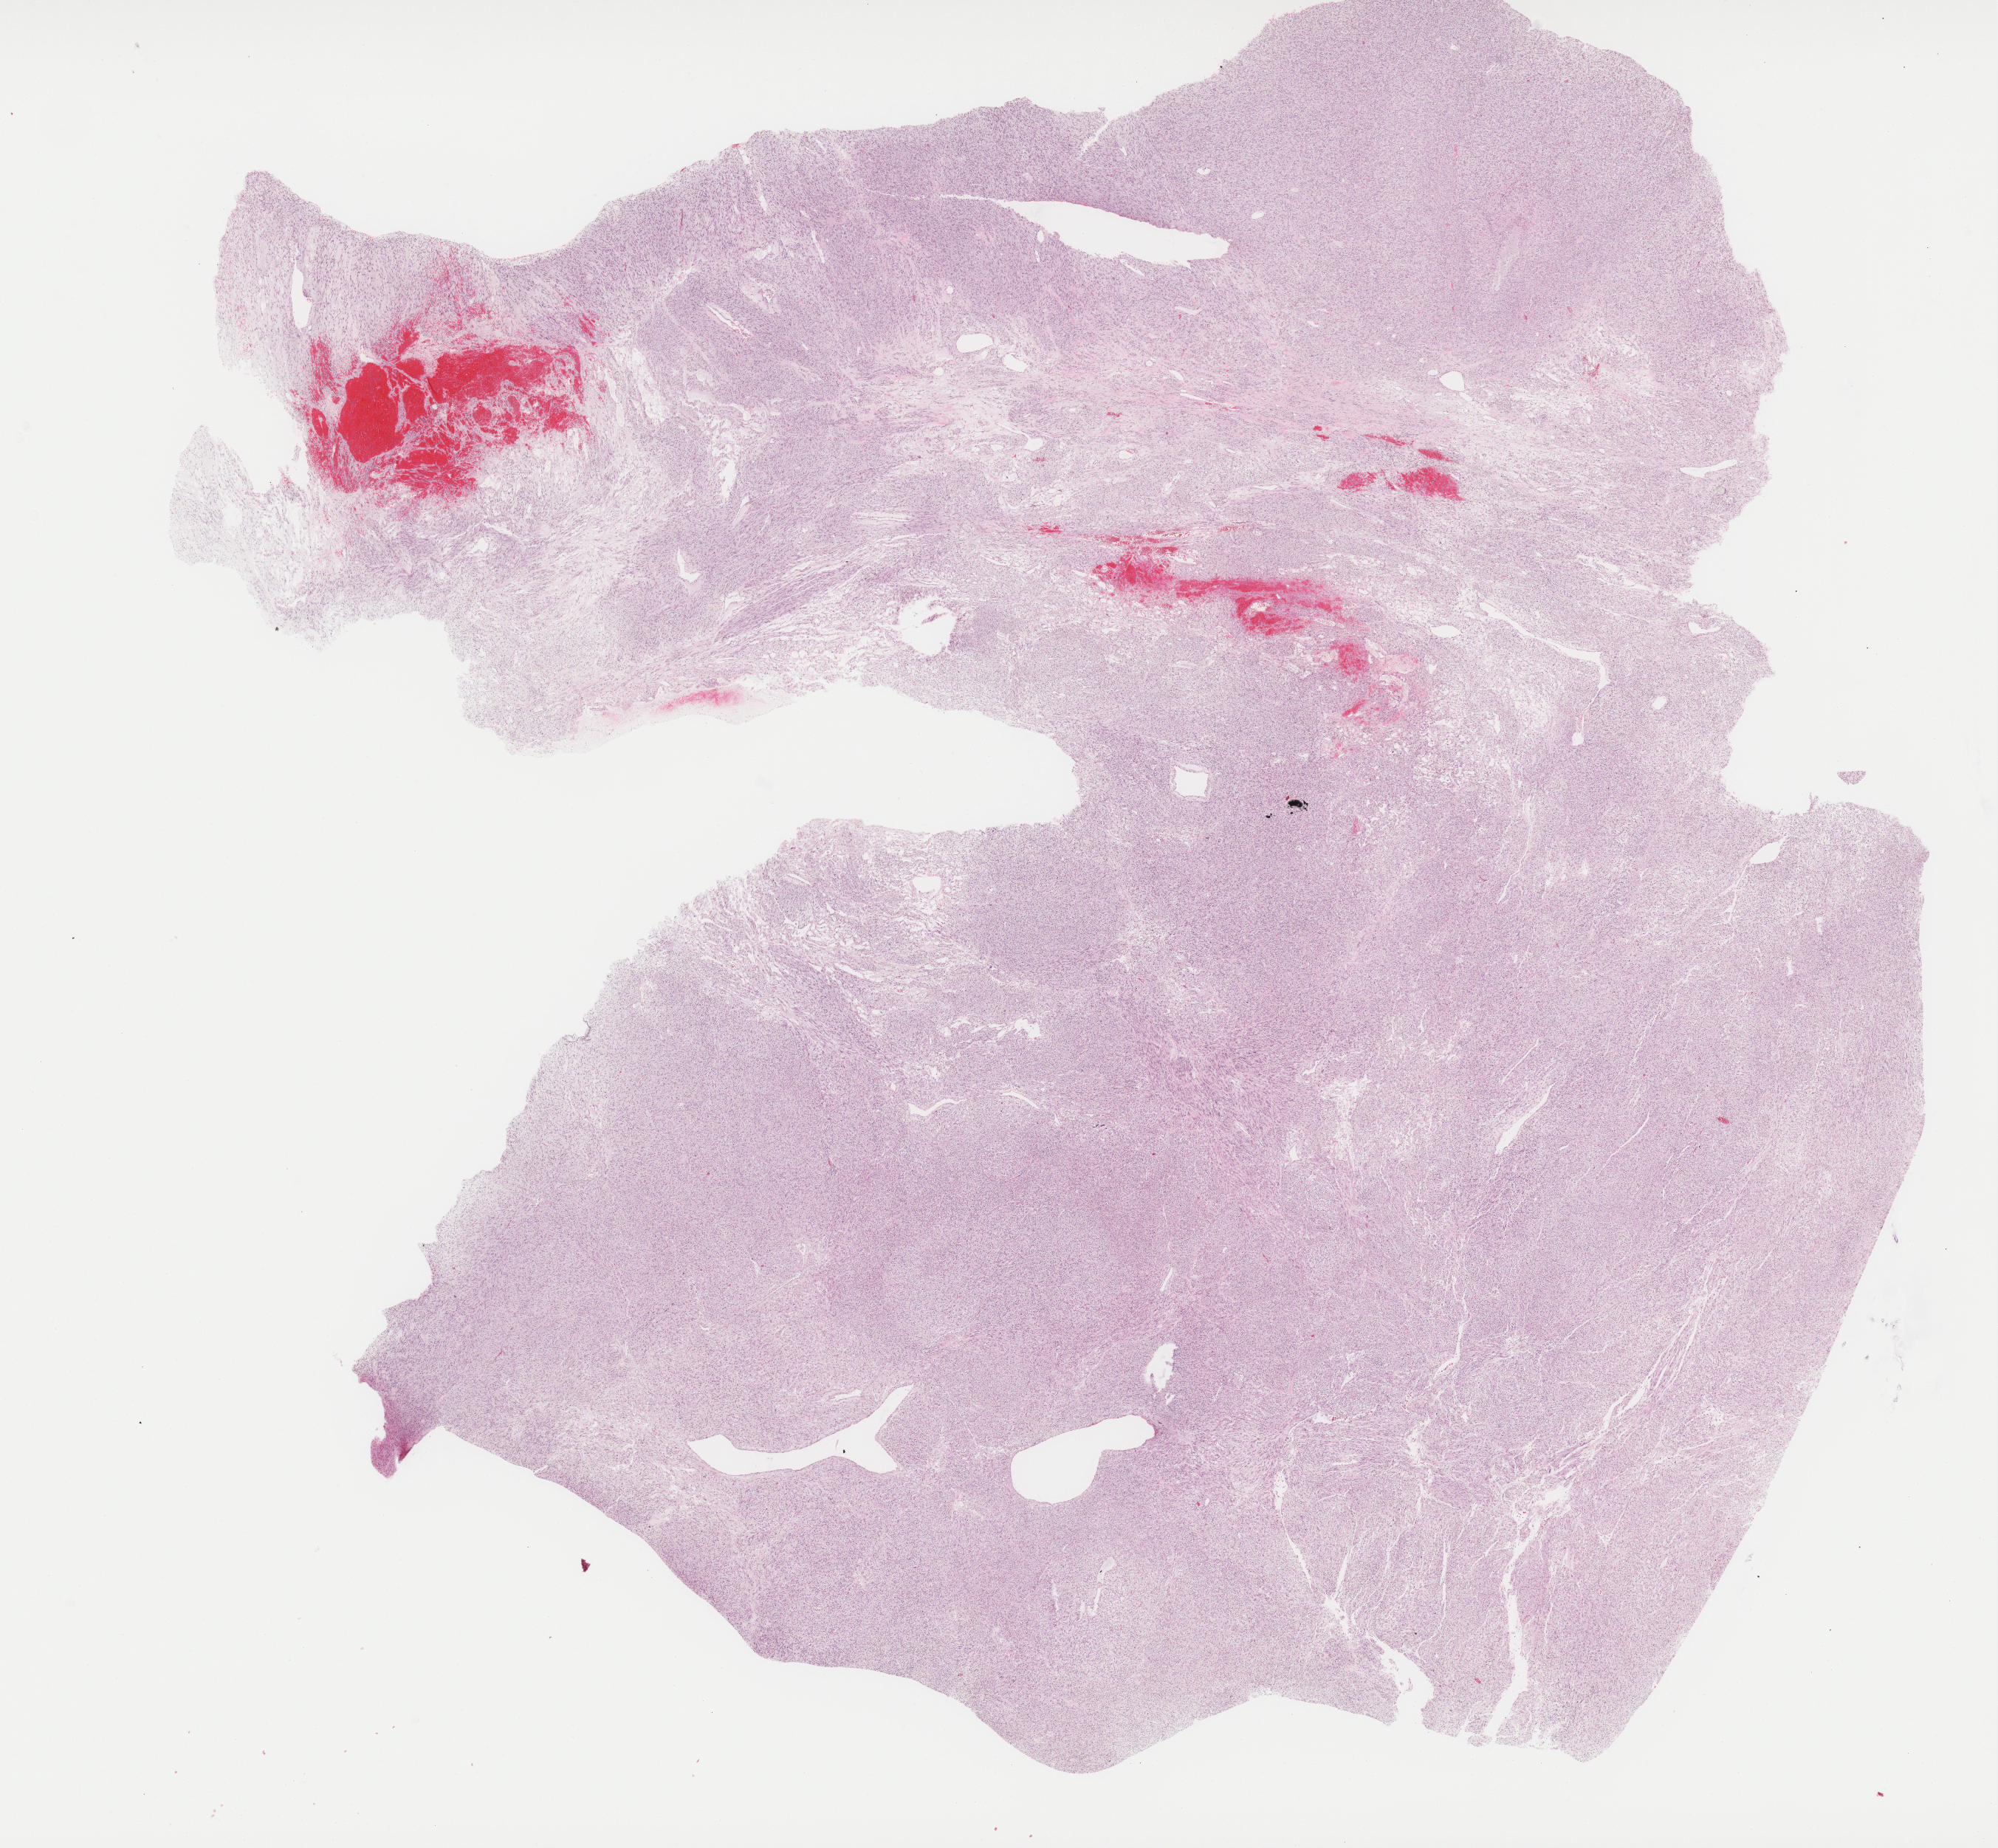
Whole-slide histology image, H&E, shown as a low-resolution overview of the whole scanned area (about 21.6 x 20.0 mm, acquisition: 40x scan); FFPE section; retroperitoneum and peritoneum, primary tumour sample. Female, age 53 years at initial diagnosis.
Histologic diagnosis: Leiomyosarcoma, NOS.